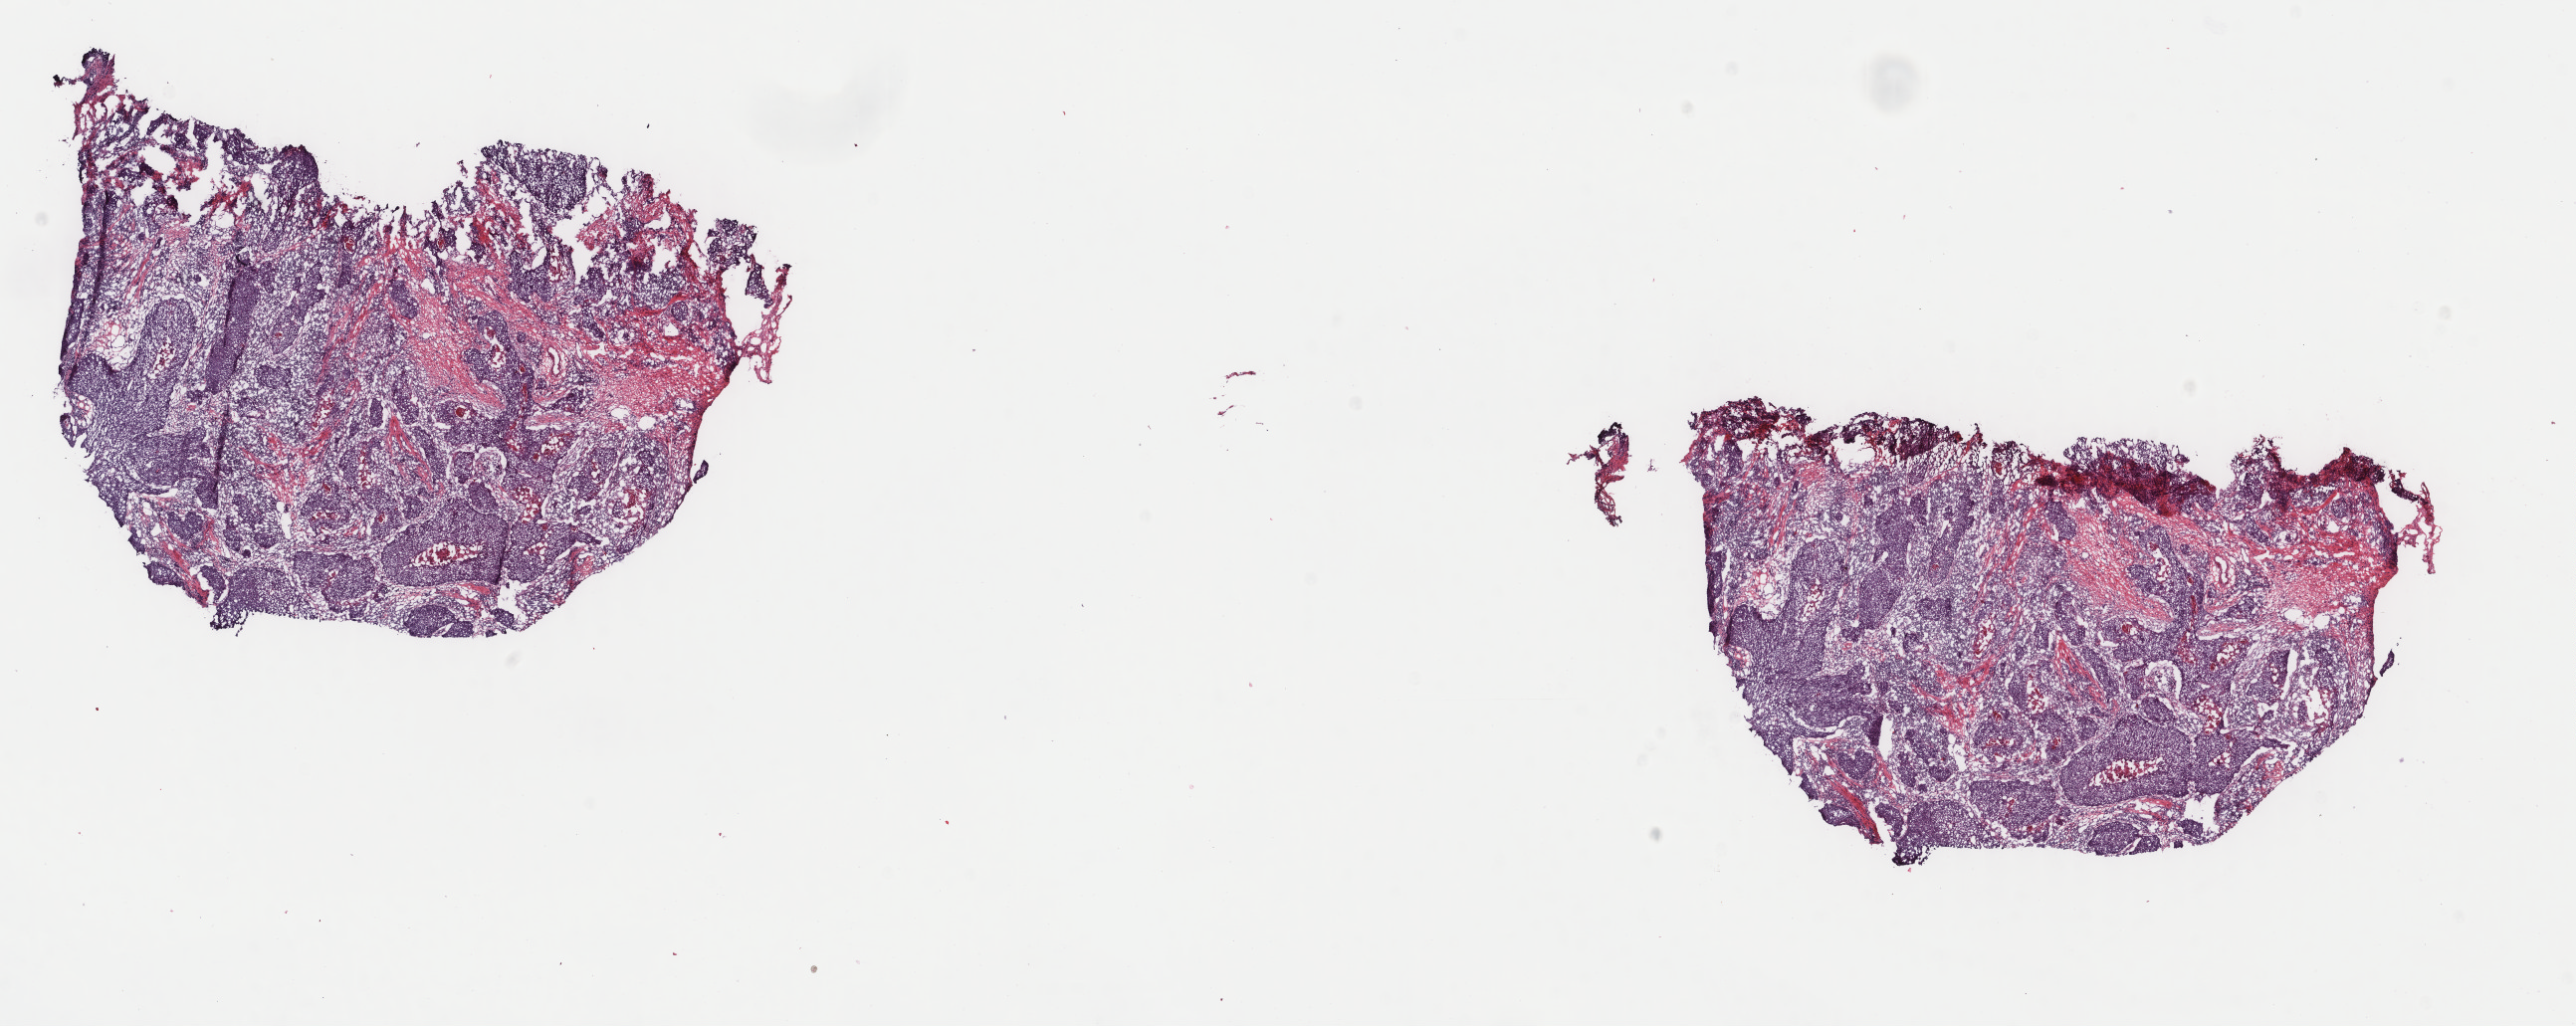
Whole-slide histology image, H&E — a low-resolution overview of the entire scanned area, about 20.5 x 8.2 mm, frozen section, primary tumour sample from the head and neck. Patient: female, age at initial diagnosis 53 years. Histologic grade: G2 (moderately differentiated). Slide review estimates, as recorded: tumour cells 70%, tumour nuclei 70%, normal cells 0%, stromal cells 30%, necrosis 0%. Inflammatory infiltration, as recorded: lymphocyte infiltration 30%, monocyte infiltration 0%, neutrophil infiltration 0%.
• laterality: right
• diagnosis: Squamous cell carcinoma, NOS (tonsil, NOS)
• AJCC pathologic stage: IVA